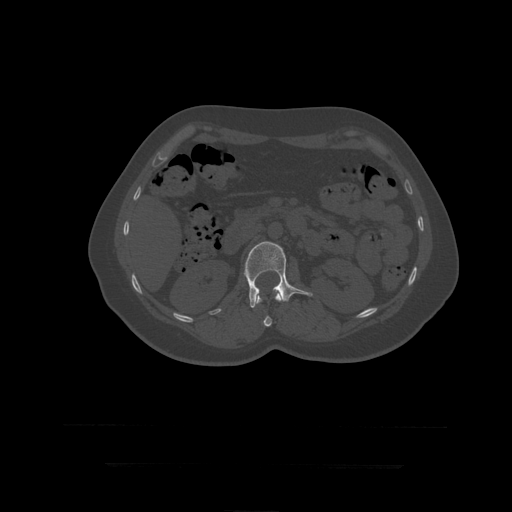
CT including the spine, one axial slice. Position 156 of 399 along the scan axis. Reconstruction kernel STANDARD. 120 kVp. Bone window (W 1800 / L 400 HU). 1.25 mm slice thickness. 512 × 512 image matrix, field of view 450 × 450 mm. Patient age 41 years. Case-level facts recorded for this patient, not image findings: primary cancer: breast.
Annotated regions visible in this slice (semi-automatically segmented with operator editing):
- L1 vertebra: bounding box [x1, y1, x2, y2] px = [256, 290, 282, 327]
- L2 vertebra: [244, 241, 313, 308]